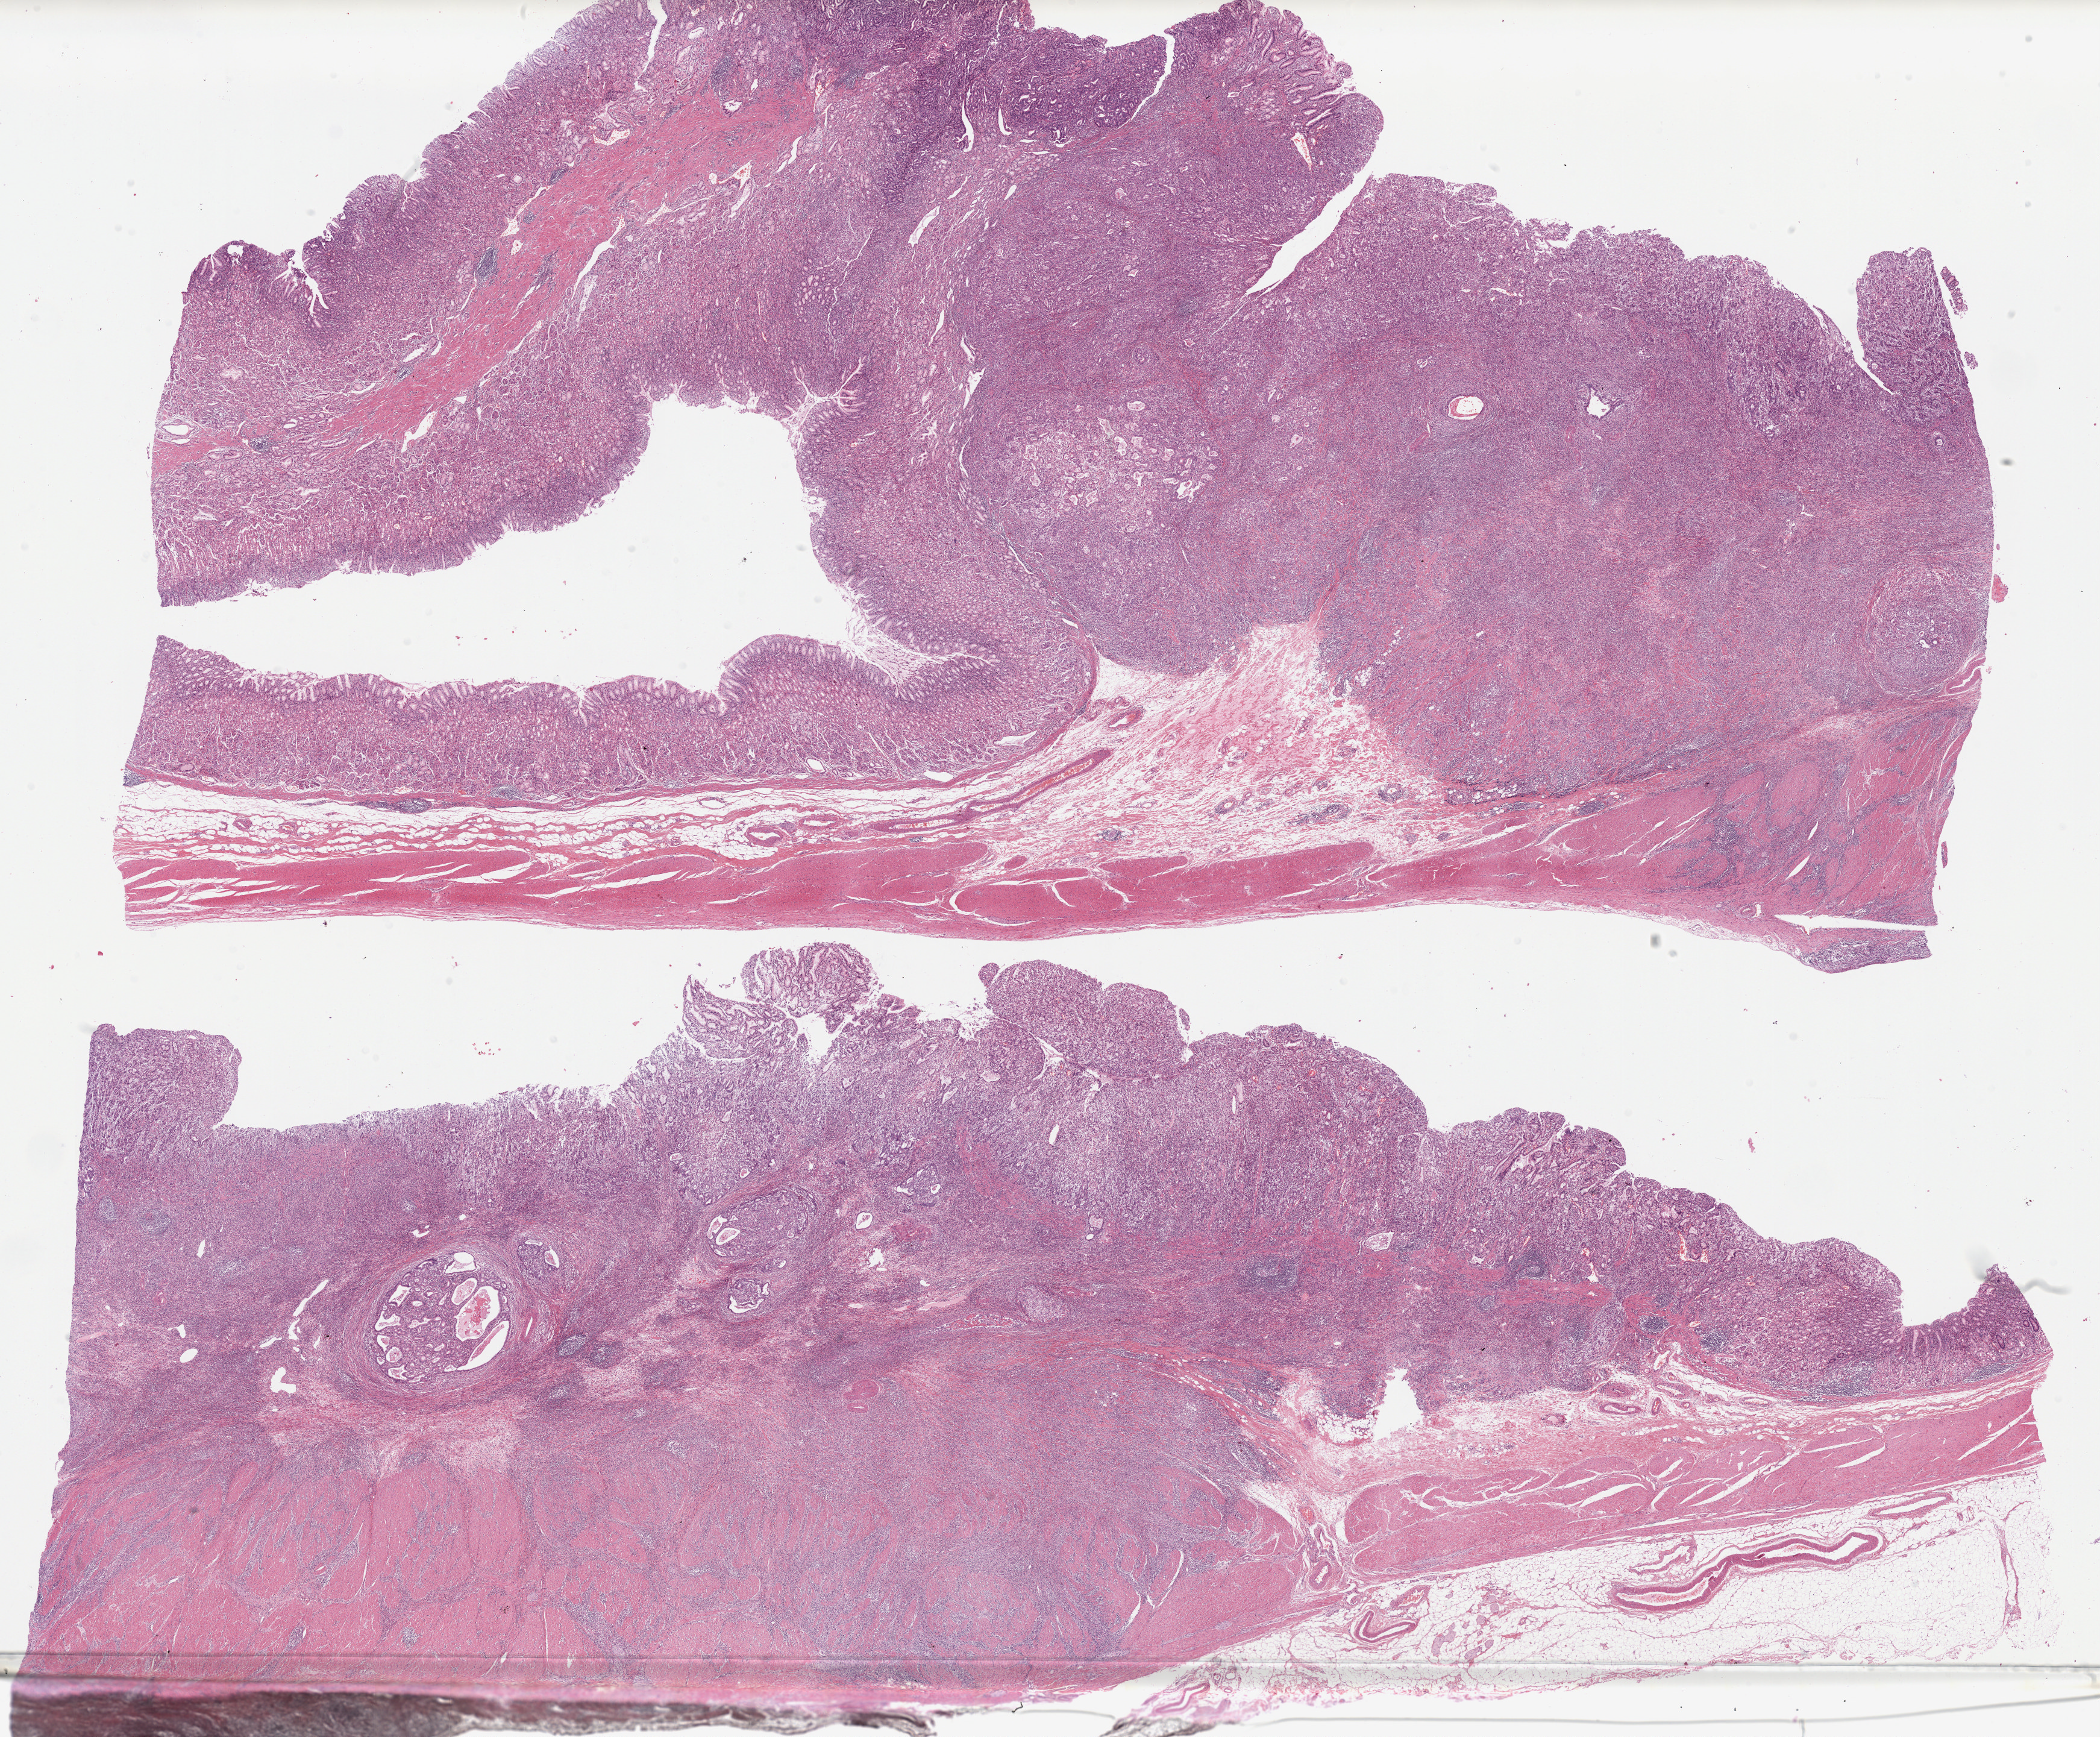
Whole-slide histology image, H&E, low-resolution overview of the scanned area, about 27.6 x 22.8 mm (from a 20x scan). Formalin-fixed paraffin-embedded (FFPE) diagnostic section. Stomach, primary tumour sample. Patient: male, age at initial diagnosis 45 years. Histologic grade: G3 (poorly differentiated).
Lymph nodes positive (case pathology): 2 of 63 examined. AJCC pathologic stage: IIB (7th edition). Diagnosis: Carcinoma, diffuse type (gastric antrum).